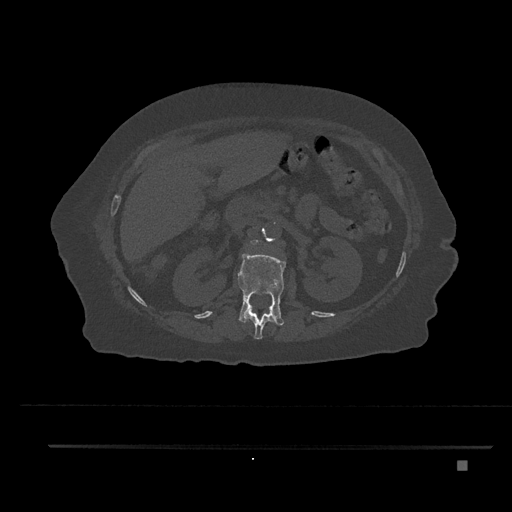
CT including the spine, one axial slice. Position 232 of 797 along the scan axis. Reconstruction kernel Br40s/3. 120 kVp. Bone window (W 1800 / L 400 HU). 0.5 mm slice thickness. 512 × 512 image matrix. Patient: female, 76 years. From the clinical record (not read from this slice): primary cancer: lung; vertebrae with lytic lesions (as recorded): T11, L3.
Outlined on this slice (semi-automatically segmented with operator editing):
- L1 vertebra: bounding box (x1, y1, x2, y2) in pixels: (237, 253, 286, 326)
- L2 vertebra: (250, 240, 259, 246)
- T12 vertebra: (244, 306, 276, 340)